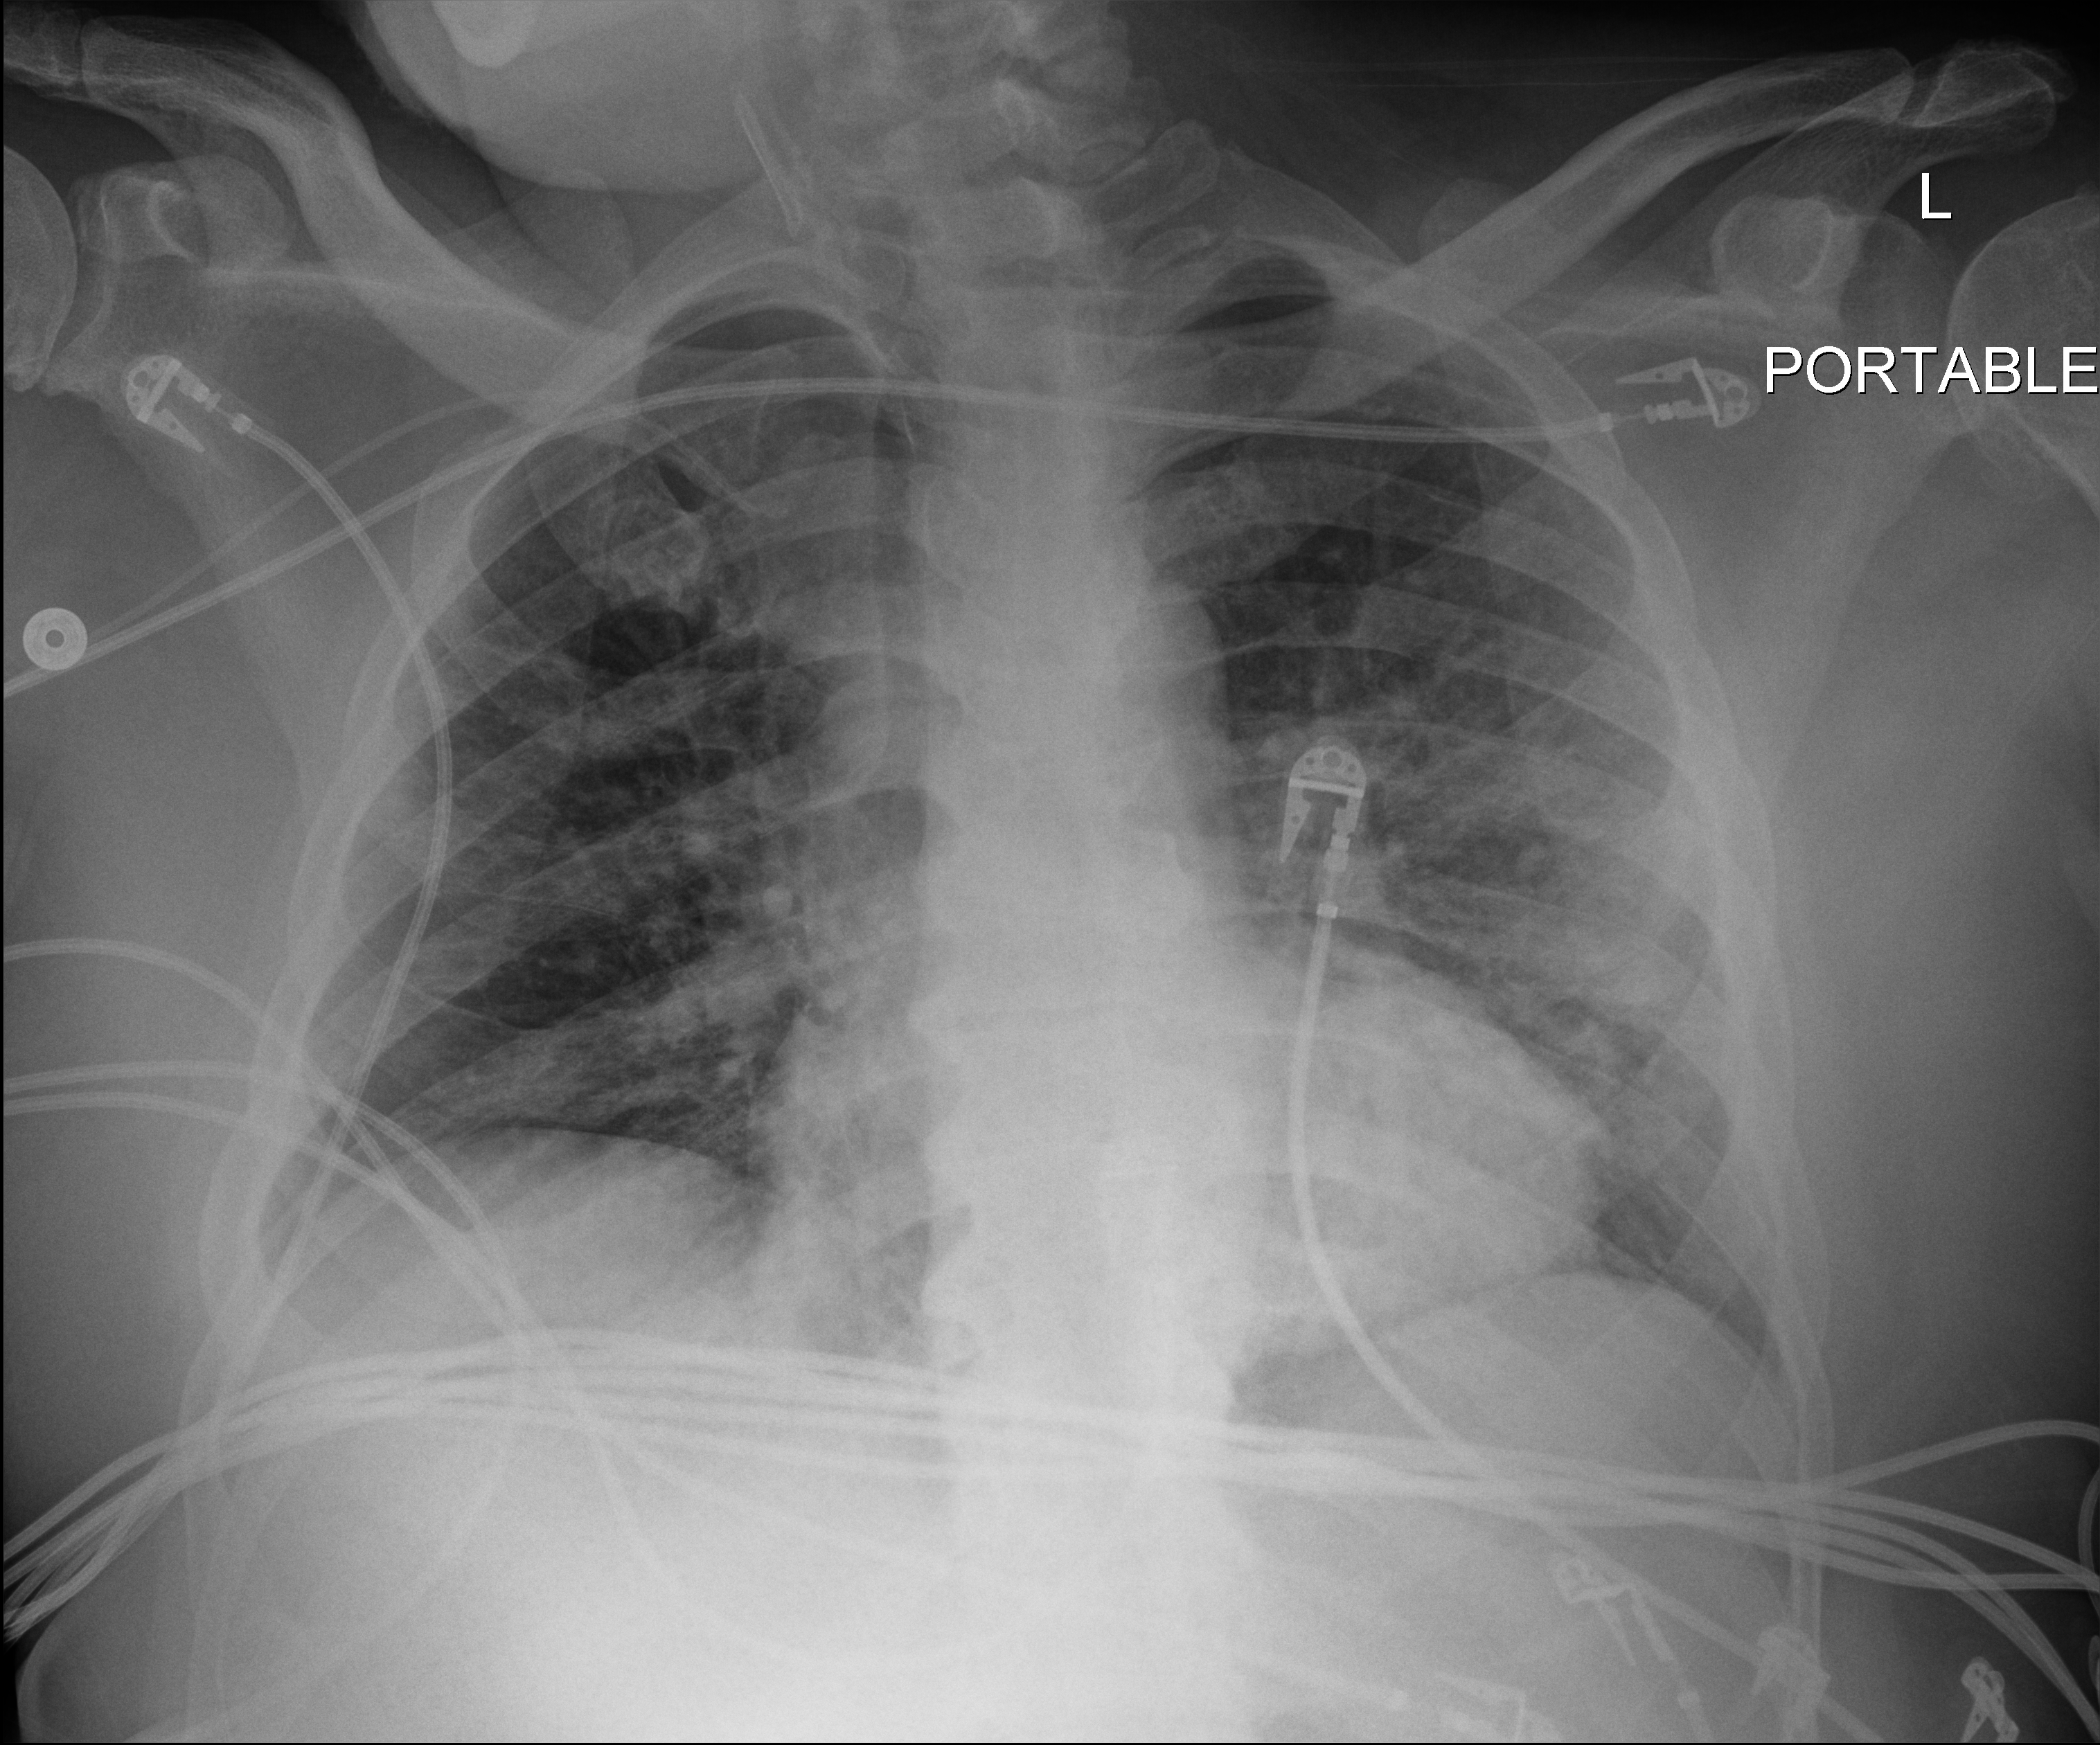
Chest X-ray (portable); anteroposterior (AP) projection. Male patient hospitalised with COVID-19, age 18–59 years.
From the hospital-stay record, not from the radiograph (when in the stay this image was taken is not recorded):
- length of hospital stay: 41 days
- chronic kidney disease (admission record): no
- admitted to intensive care during this hospital stay: yes